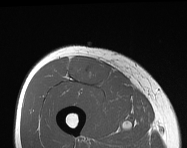
MRI of an extremity soft-tissue mass, one axial slice; position 58 of 114 along the scan axis; MR volume resampled by the dataset authors to the PET/CT grid (not the native acquisition matrix); 3.27 mm slice thickness; 187 × 148 image matrix, field of view 183 × 145 mm. Male patient. From the clinical record (not read from this slice): histological type: pleiomorphic leiomyosarcoma; grade: intermediate; site of the primary tumour: right thigh.
Outlined on this slice (expert contour drawn on MRI and transferred to this co-registered scan by the dataset authors):
- gross tumour volume including surrounding oedema: box from (x=70, y=56) to (x=113, y=87) px